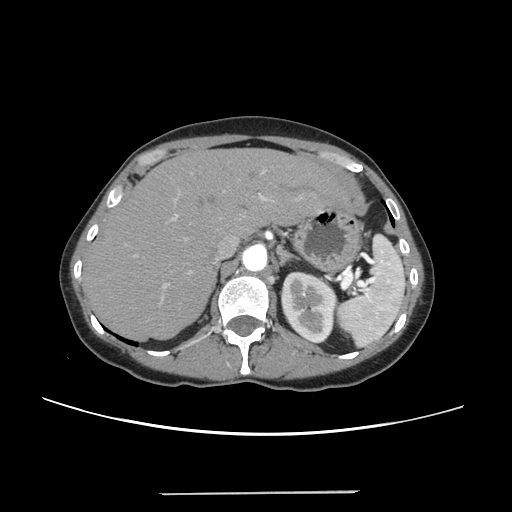
Contrast-enhanced abdominal CT, one axial slice; slice 175 of 240 in the series (ordered by position); 120 kVp; soft-tissue window (W 400 / L 40 HU); 512 × 512 image matrix, field of view 371 × 371 mm. Female patient, age 60 years. From the clinical record (not read from this slice): diagnosis: colorectal cancer liver metastases, imaged before liver resection; multiple liver metastases: no; largest metastasis: 1.5 cm; disease in both lobes: no.
Outlined on this slice (expert manual segmentation):
- liver: box from (x=86, y=150) to (x=348, y=339) px
- planned liver remnant (the part of the liver to remain after resection): (x=86, y=150)–(x=349, y=339)
- portal vein (with intrahepatic branches): (x=134, y=171)–(x=303, y=288)